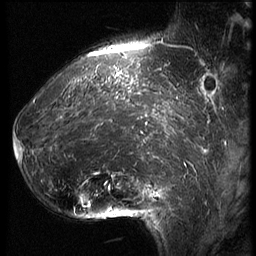
Breast MRI (dynamic contrast-enhanced), one sagittal slice; position 18 of 62 along the scan axis; 3 images stored at this slice position (order not interpretable as contrast timing); 1.5 T; TE 4.2 ms, TR 9 ms; 2.5 mm slice thickness; 256 × 256 image matrix, field of view 180 × 180 mm. Female patient, age 39 years. From the clinical record (not read from this slice): setting: breast cancer imaged before/during neoadjuvant chemotherapy; receptor status: HER2-positive.
Structures marked on this image (semi-automatic segmentation, software-assisted and operator-edited):
- analysis volume of interest (the breast-tissue region the enhancement analysis was run in; not a lesion): bounding box [x1, y1, x2, y2] px = [16, 64, 171, 228]
- tumour enhancement mask (voxels above the 140 % enhancement threshold inside the analysis volume of interest): [16, 72, 170, 205]